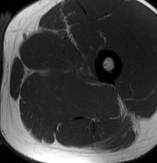
MRI of an extremity soft-tissue mass, one axial slice; slice 50 of 70 in the series (ordered by position); MR volume resampled by the dataset authors to the PET/CT grid (not the native acquisition matrix); 157 × 163 image matrix, field of view 153 × 159 mm. Male patient. From the clinical record (not read from this slice): histological type: extraskeletal osteosarcoma; grade: high; site of the primary tumour: left adductur.
Annotated regions visible in this slice (expert contour drawn on MRI and transferred to this co-registered scan by the dataset authors):
- gross tumour volume (mass): bounding box [x1, y1, x2, y2] px = [33, 60, 121, 120]